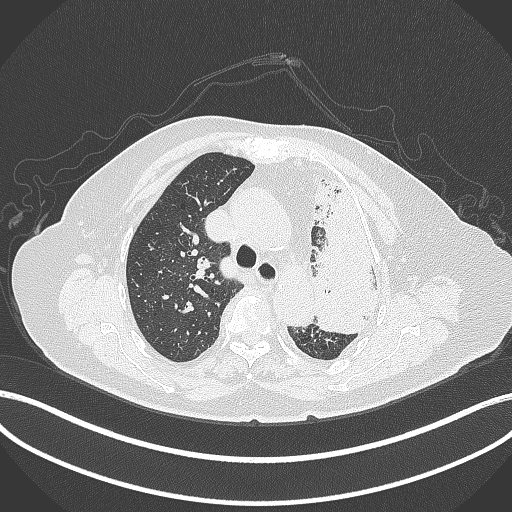
Chest CT, one axial slice. Position 283 of 399 along the scan axis. 120 kVp. Lung window (W 1500 / L -600 HU). 1 mm slice thickness. 512 × 512 image matrix. Female patient, age 75 years. Case-level facts recorded for this patient, not image findings: clinical TNM (as recorded): T3 N3 M1.
Annotated regions visible in this slice (bounding box drawn by a radiologist):
- lung tumour (recorded histology: adenocarcinoma): bounding box <303,151,390,334> (left, top, right, bottom; pixels)